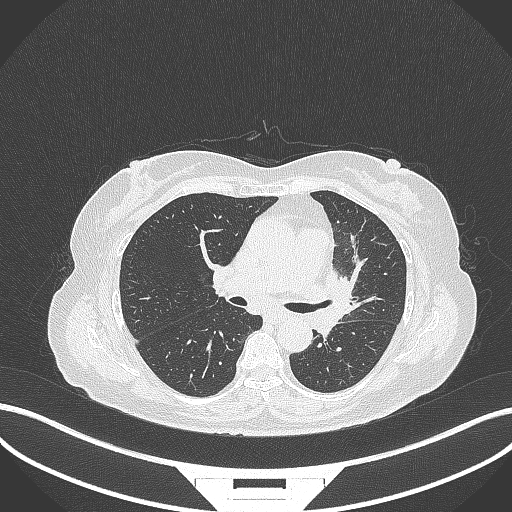
Chest CT, one axial slice; slice 193 of 382 in the series (ordered by position); 120 kVp; lung window (W 1500 / L -600 HU); 1 mm slice thickness; 512 × 512 image matrix, field of view 400 × 400 mm. Patient: female, 64 years. From the clinical record (not read from this slice): clinical TNM (as recorded): T2a N2 M0.
Annotated regions visible in this slice (bounding box drawn by a radiologist):
- lung tumour (recorded histology: adenocarcinoma): bounding box (x1, y1, x2, y2) in pixels: (314, 266, 355, 336)